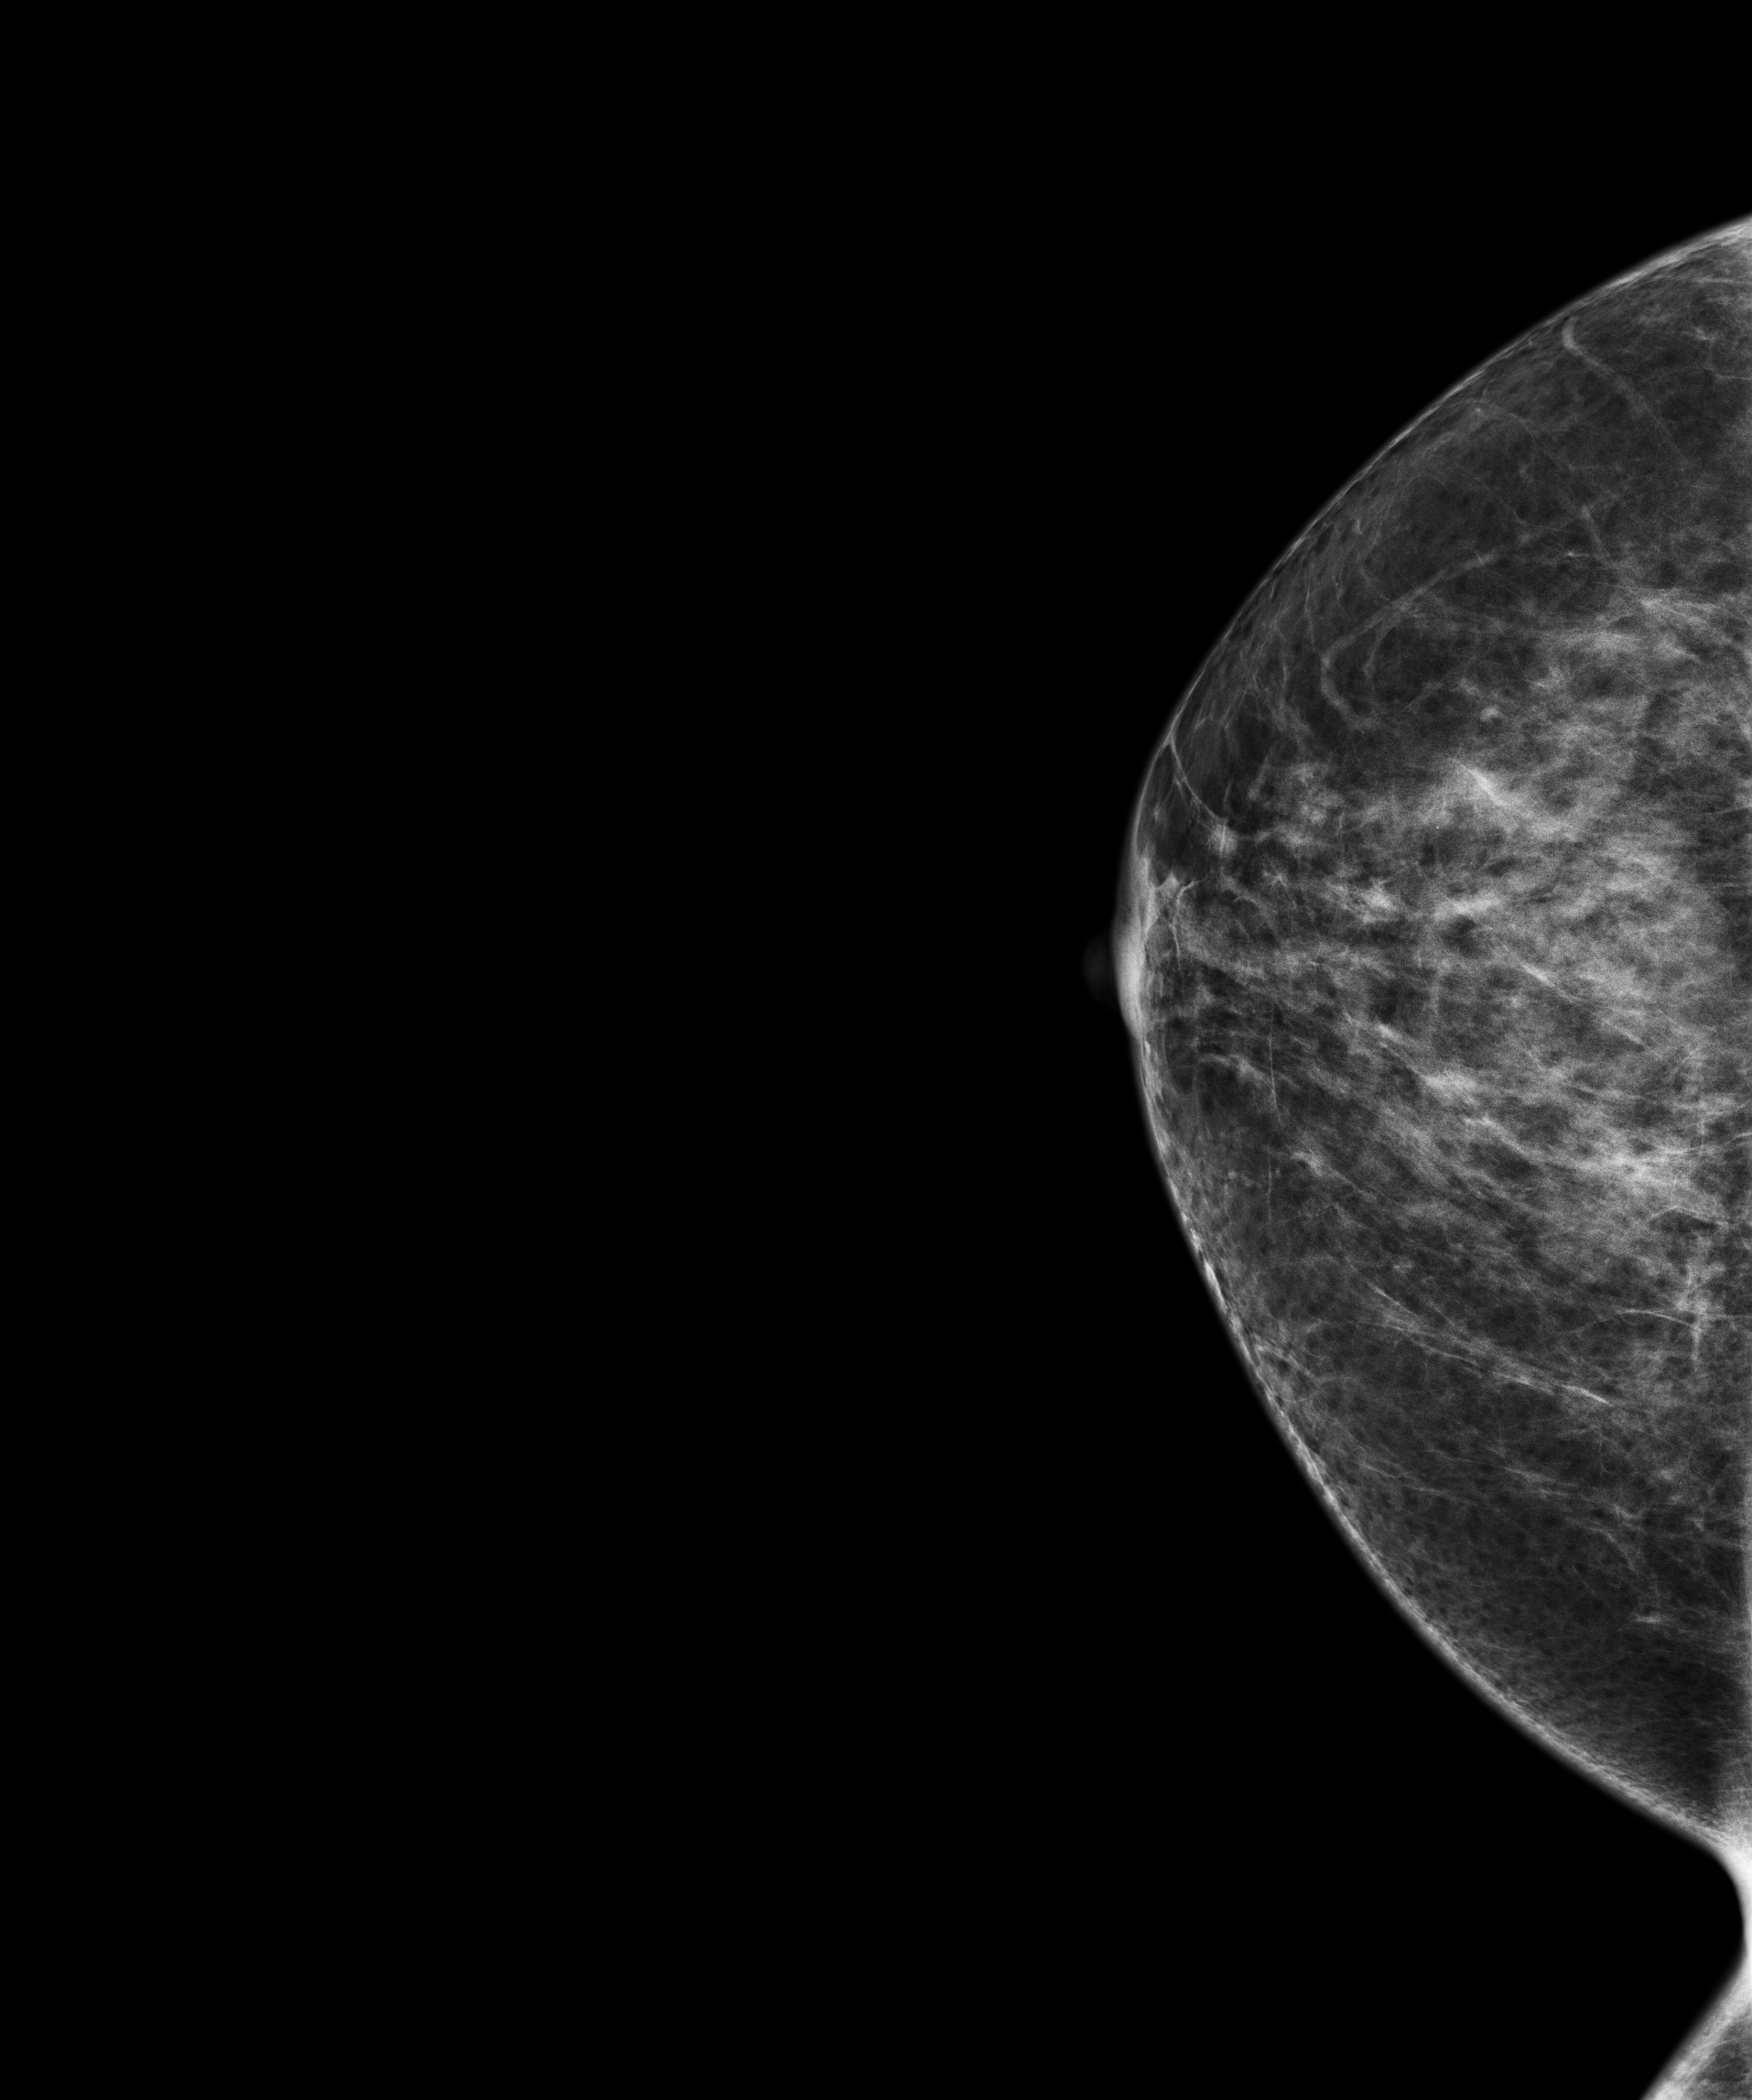
Annual screening mammography examination, compressed breast thickness 56.2 mm. Patient: female, 49 years.
Image type: full-field digital mammogram. Breast: right. Projection: craniocaudal (CC) view.